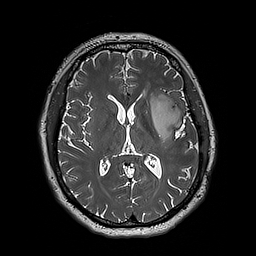
Brain MRI from a brain-tumour surgery series, one axial slice; position 99 of 192 along the scan axis; 1 mm slice thickness; 256 × 256 image matrix, field of view 250 × 250 mm. From the clinical record (not read from this slice): histopathology: Astrocytoma; WHO grade: 3; IDH mutation: yes.
Outlined on this slice (expert manual segmentation):
- tumour: box from (x=150, y=95) to (x=184, y=142) px